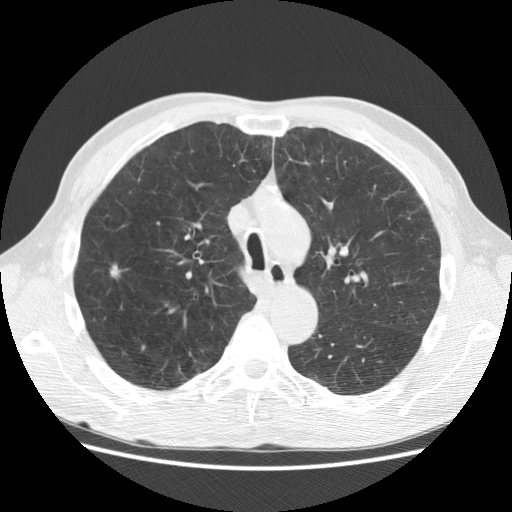
Chest CT (low-dose screening protocol), one axial image; baseline annual screen; lung window (W 1500 / L -600 HU). Male participant, aged 62 years at enrolment. Current smoker at enrolment.
Expert reader's lesion annotation, bounding box <102,260,135,291> (left, top, right, bottom; pixels). The screening reader recorded 2 non-calcified nodules or masses ≥4 mm on this exam (right upper lobe, left lower lobe); which of them this box marks is not recorded. Official screen result: positive, change unspecified: nodule(s) >= 4 mm or enlarging nodule(s), mass(es), or other non-specific abnormalities suspicious for lung cancer.